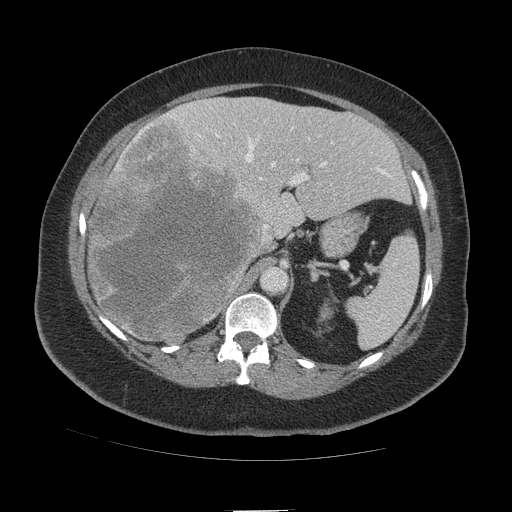
Contrast-enhanced abdominal CT (liver protocol), one axial slice. Position 67 of 109 along the scan axis. Reconstruction kernel STANDARD. Soft-tissue window (W 400 / L 40 HU). 2.5 mm slice thickness. 512 × 512 image matrix, field of view 420 × 420 mm. From the clinical record (not read from this slice): diagnosis: hepatocellular carcinoma (patient treated with transarterial chemoembolisation; whether this scan precedes or follows treatment is not stated here); TNM stage (as recorded): Stage-IVB; Child-Pugh class: A; tumour differentiation: poorly differentiated.
Outlined on this slice (semi-automatic segmentation, software-assisted and operator-edited):
- liver parenchyma outside the tumour (the mass and vessels are separate outlines, so this box may not span the whole liver): box from (x=88, y=96) to (x=410, y=338) px
- mass: (x=89, y=119)–(x=265, y=345)
- liver vessels: (x=134, y=114)–(x=391, y=229)